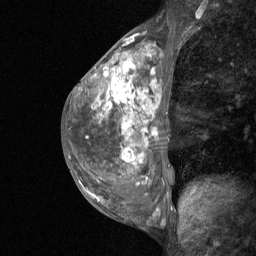
Breast MRI (dynamic contrast-enhanced), one sagittal slice. Position 28 of 64 along the scan axis. Dynamic contrast-enhanced study with each time point stored as its own series, time point 2 of 3 at this slice position (early post-contrast, ordered by acquisition time). 1.5 T. TE 4.8 ms, TR 27 ms. 2 mm slice thickness. 256 × 256 image matrix, field of view 200 × 200 mm. Female patient, age 36 years. Case-level facts recorded for this patient, not image findings: setting: breast cancer imaged before/during neoadjuvant chemotherapy; receptor status: HR-positive, HER2-negative.
Structures marked on this image (semi-automatic segmentation, software-assisted and operator-edited):
- analysis volume of interest (the breast-tissue region the enhancement analysis was run in; not a lesion): bounding box (x1, y1, x2, y2) in pixels: (73, 45, 171, 210)
- tumour enhancement mask (voxels above the 90 % enhancement threshold inside the analysis volume of interest): (115, 67, 126, 80)